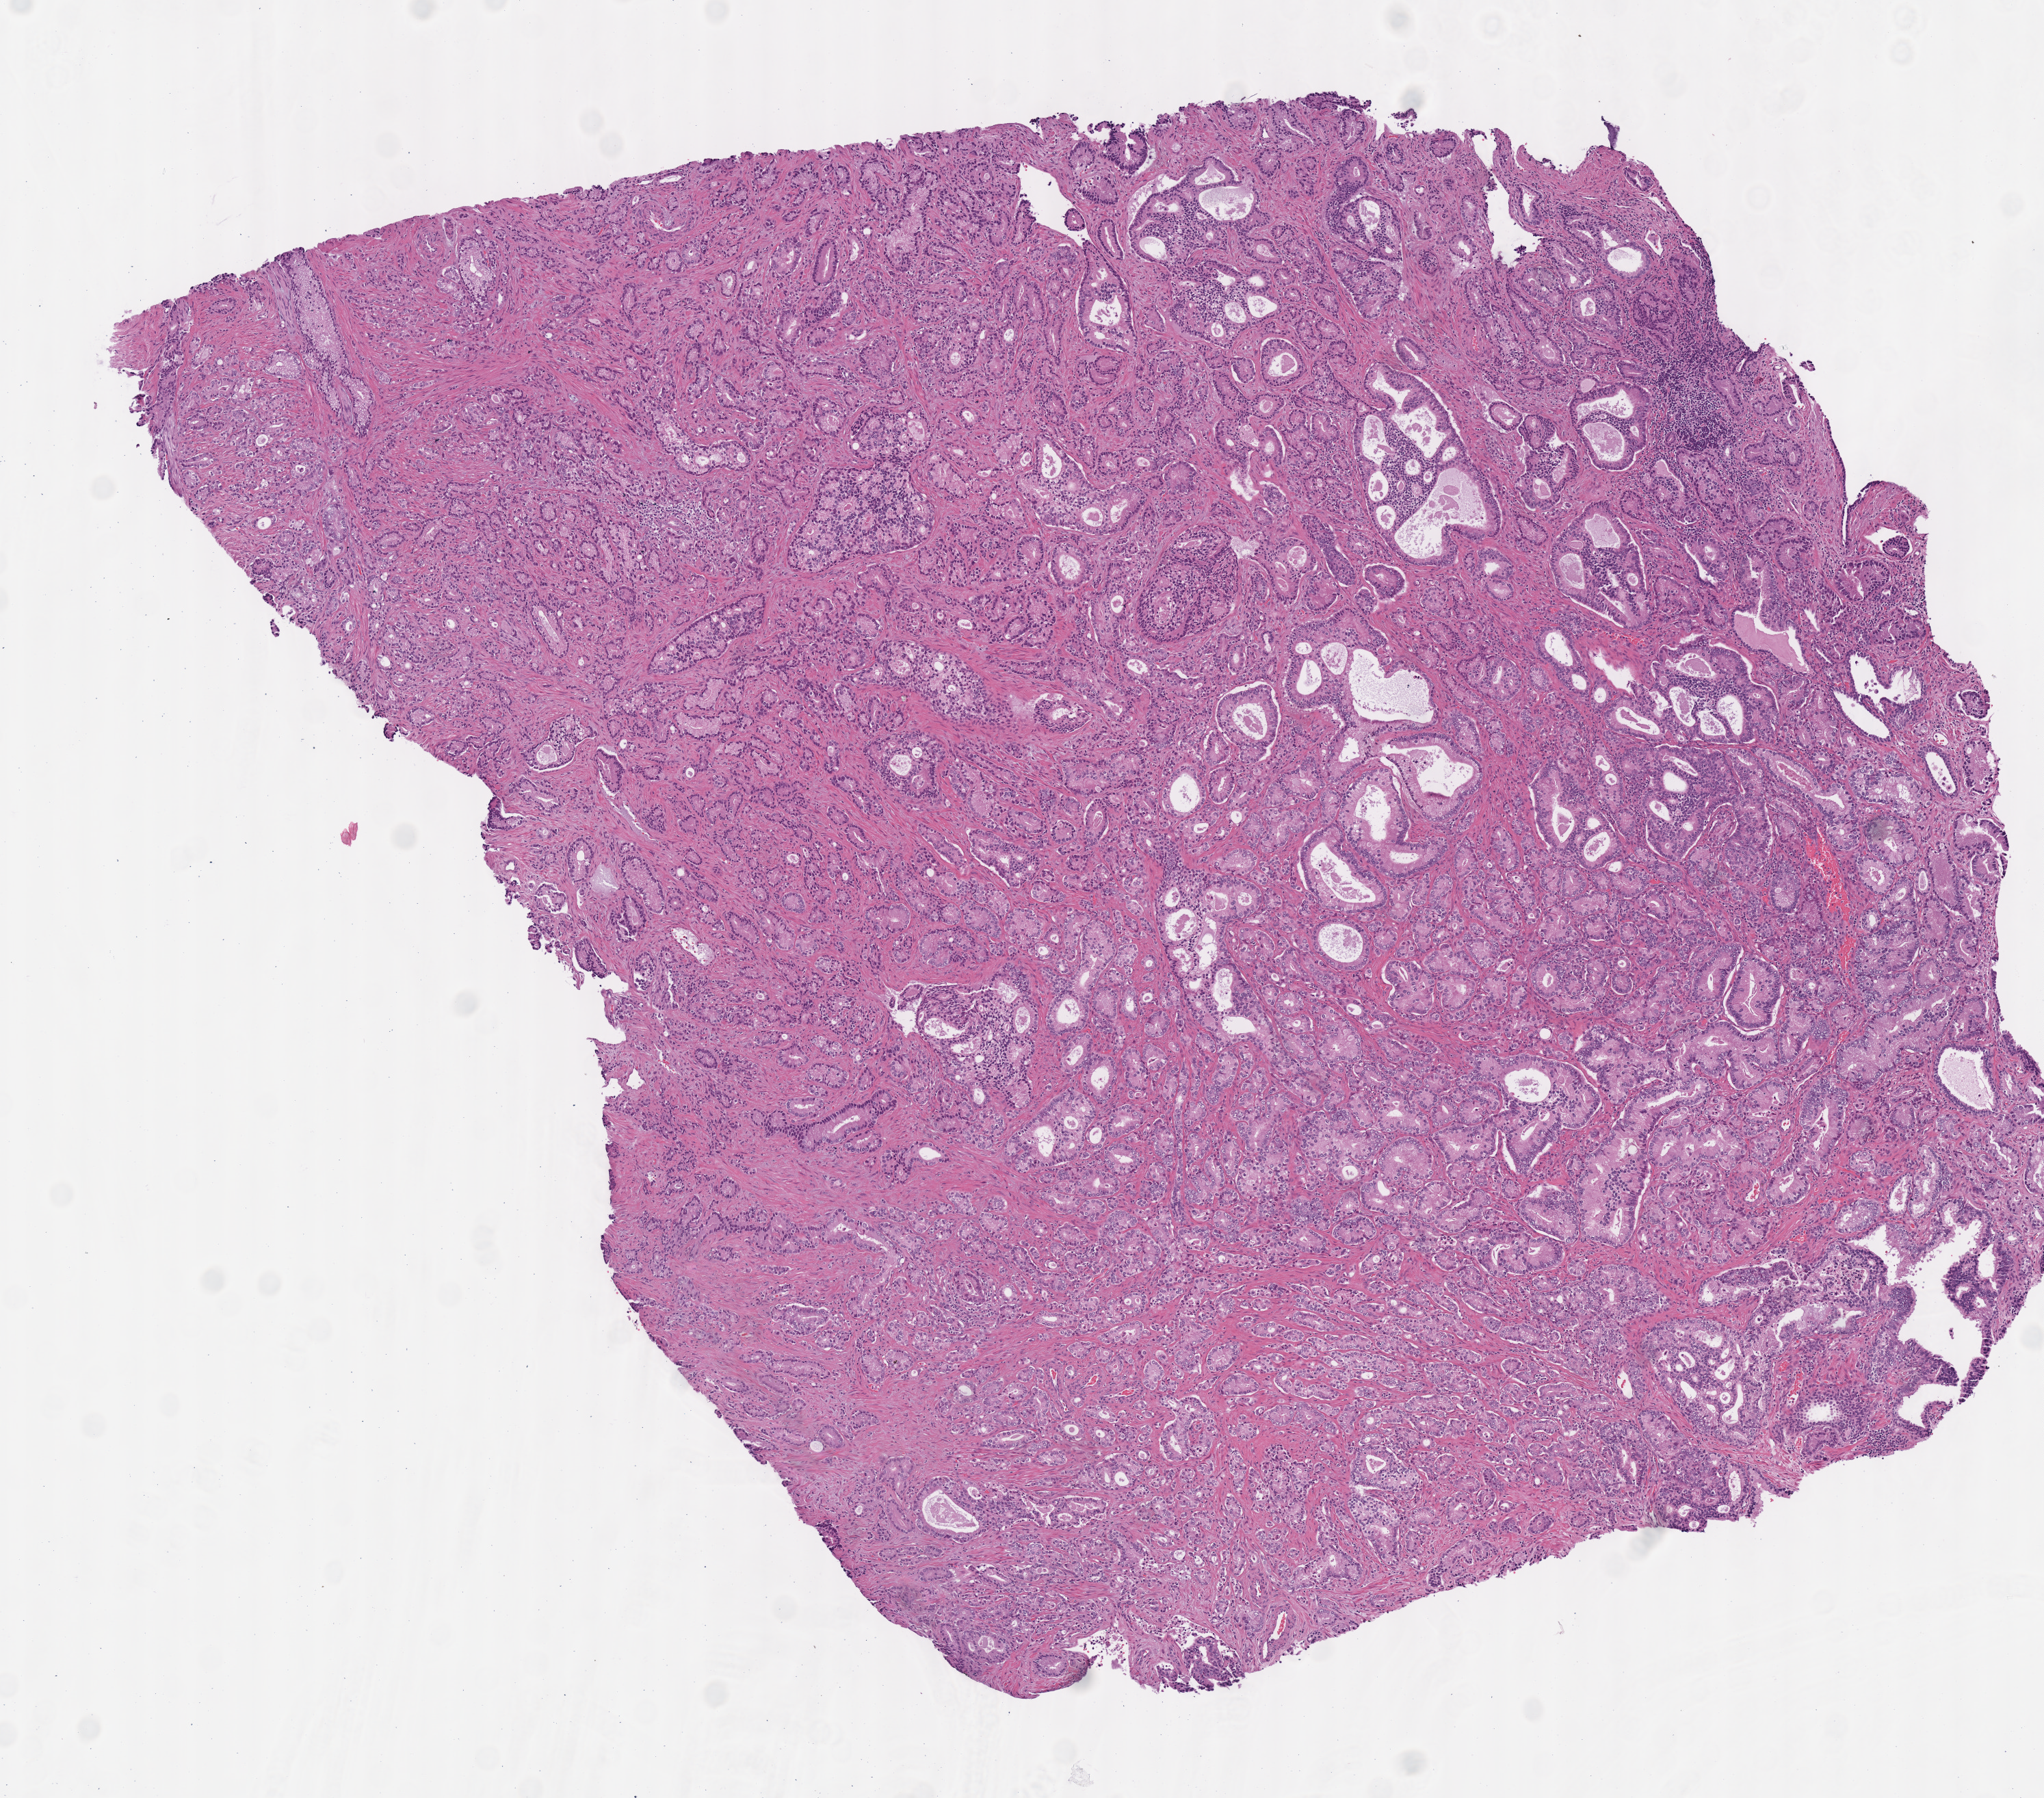
Whole-slide histology image, H&E-stained — shown as a low-resolution overview of the whole scanned area (about 5.9 x 5.2 mm, acquisition: 40x scan). Frozen section from the top of the tissue portion. Primary tumour sample from the prostate. Male patient; age at initial diagnosis 66 years. Gleason score: 8 (3+5). Pathologist review of this section (percent, as recorded): tumour cells 0%, tumour nuclei 80%, normal cells 0%, stromal cells 0%, necrosis 0%.
Lymph nodes positive (case pathology): 0 of 8 examined. Diagnosis: Acinar cell carcinoma.